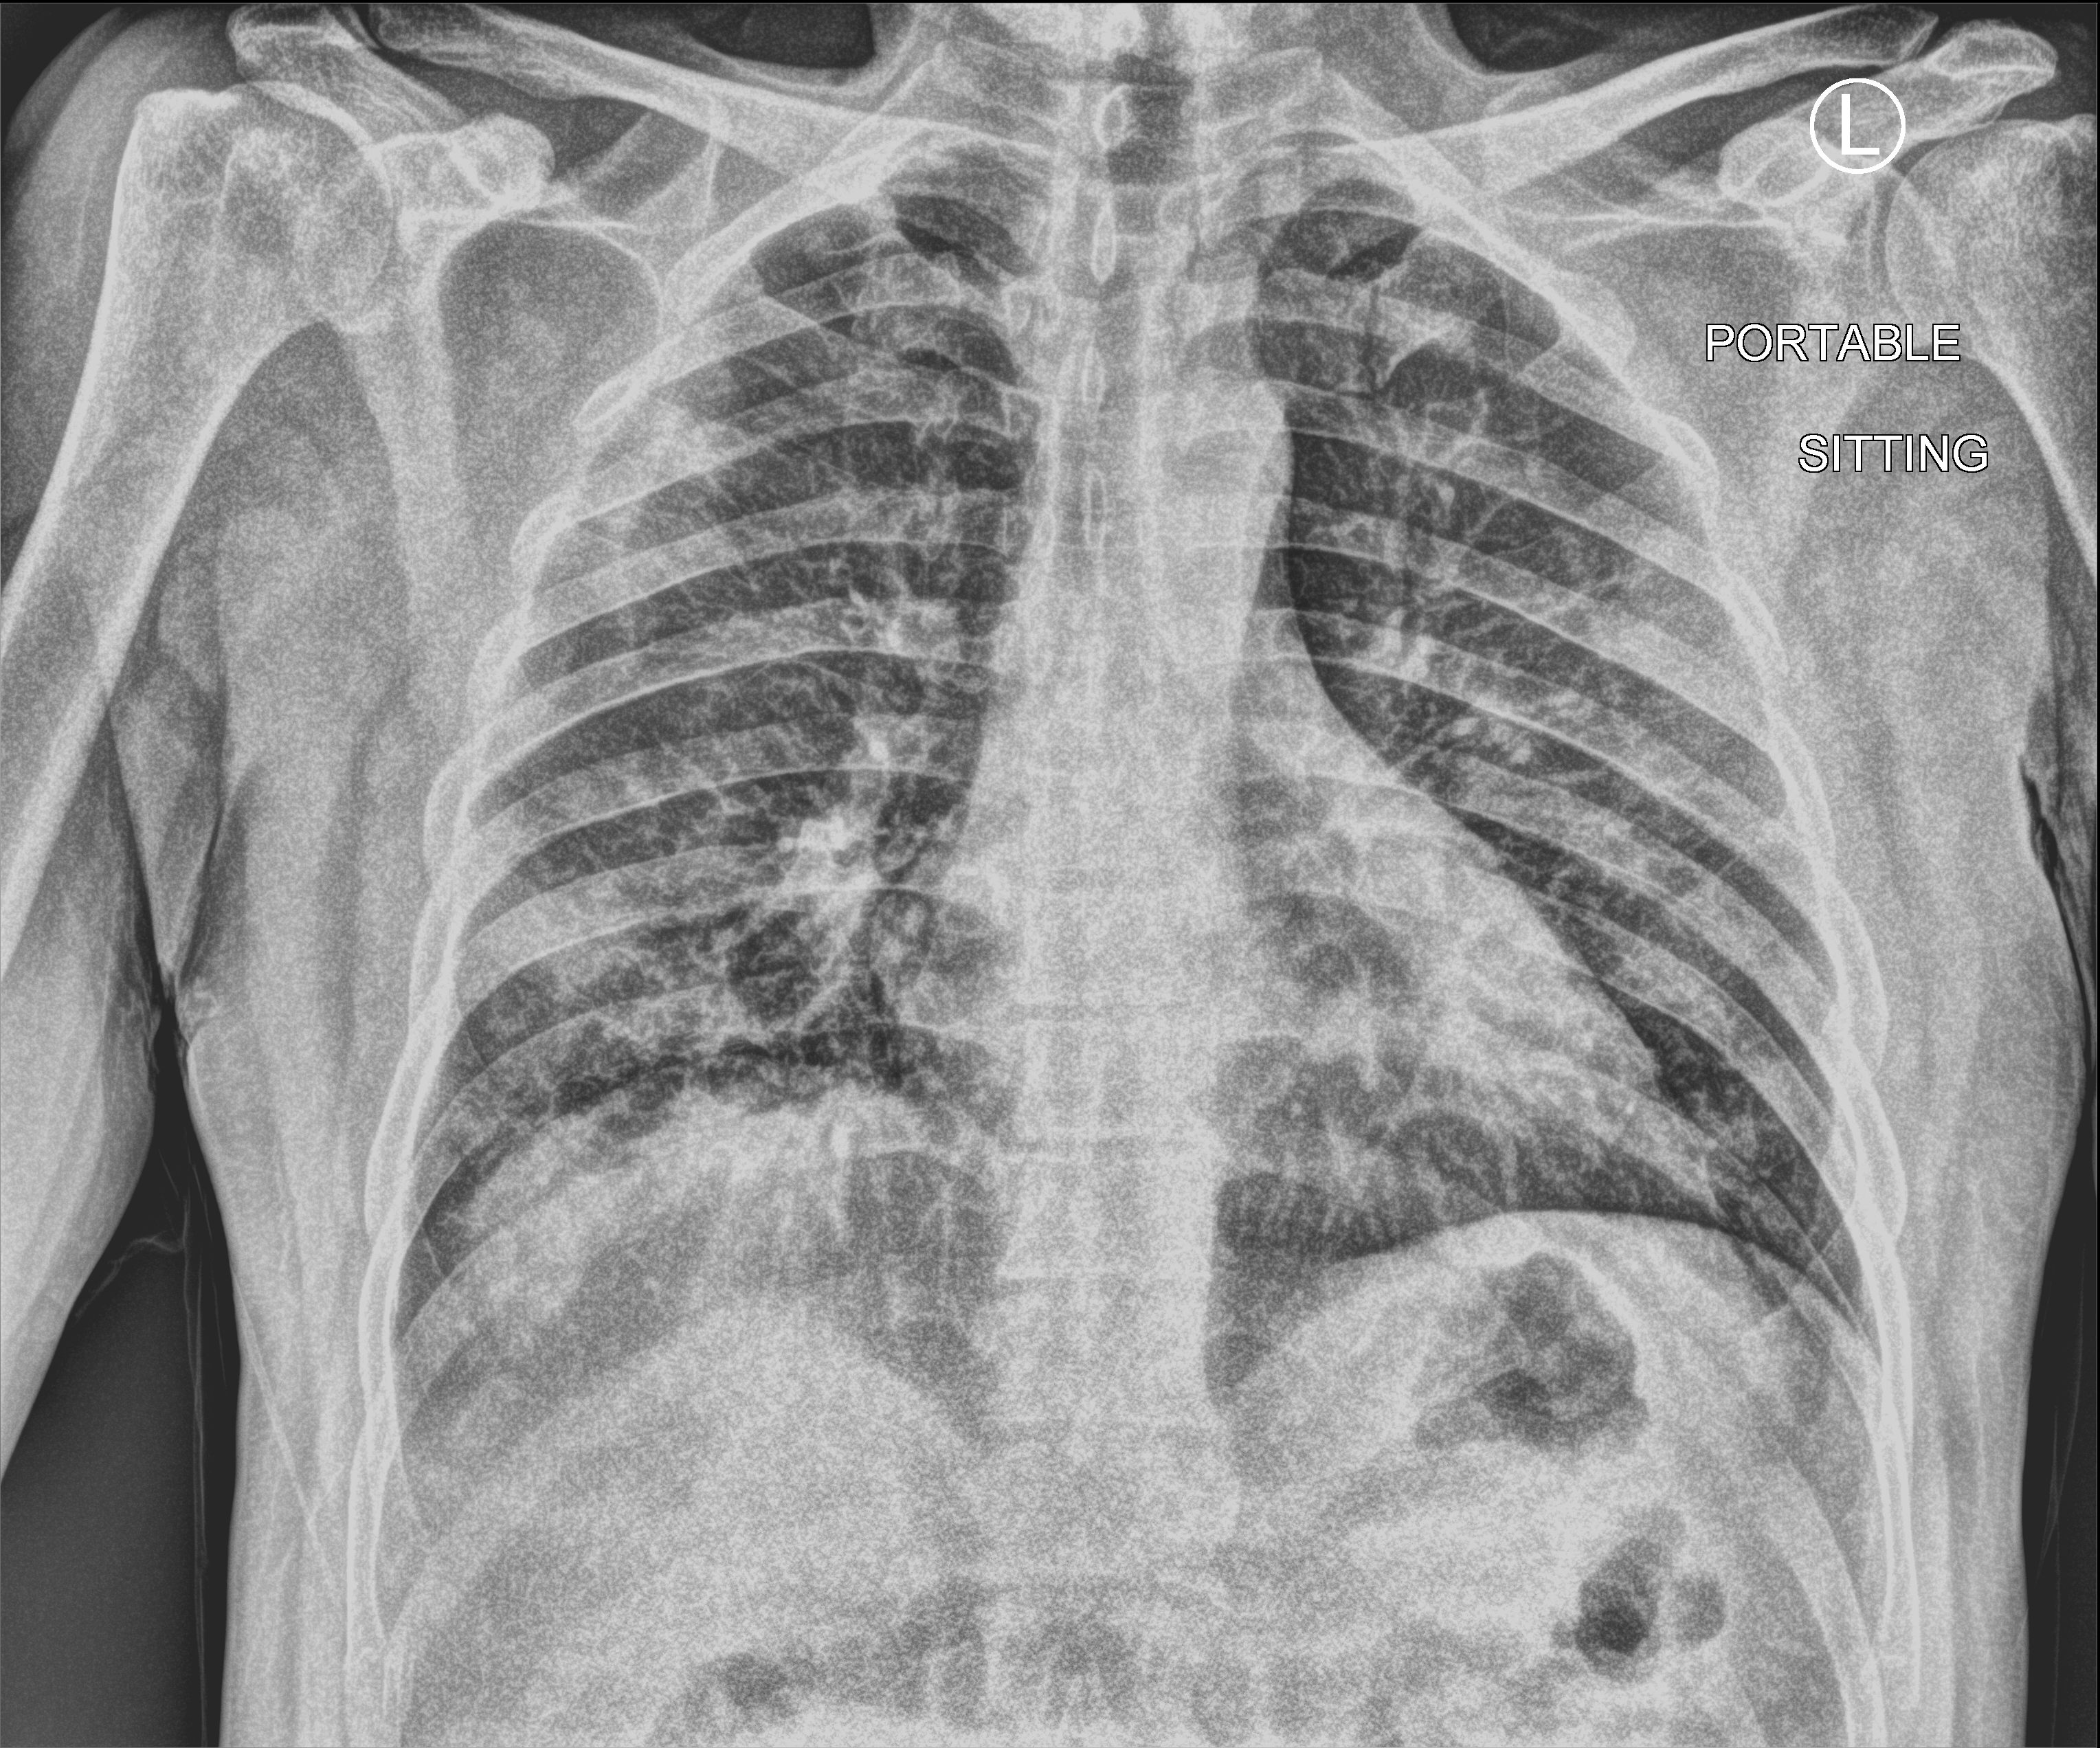
Portable chest radiograph; anteroposterior (AP) projection. Male patient hospitalised with COVID-19, age 18–59 years.
Hospital-stay facts (about this admission, not read from this image; timing relative to this image not recorded): admitted to intensive care during this hospital stay: no; mechanically ventilated during this hospital stay: no; length of hospital stay: 1 day.